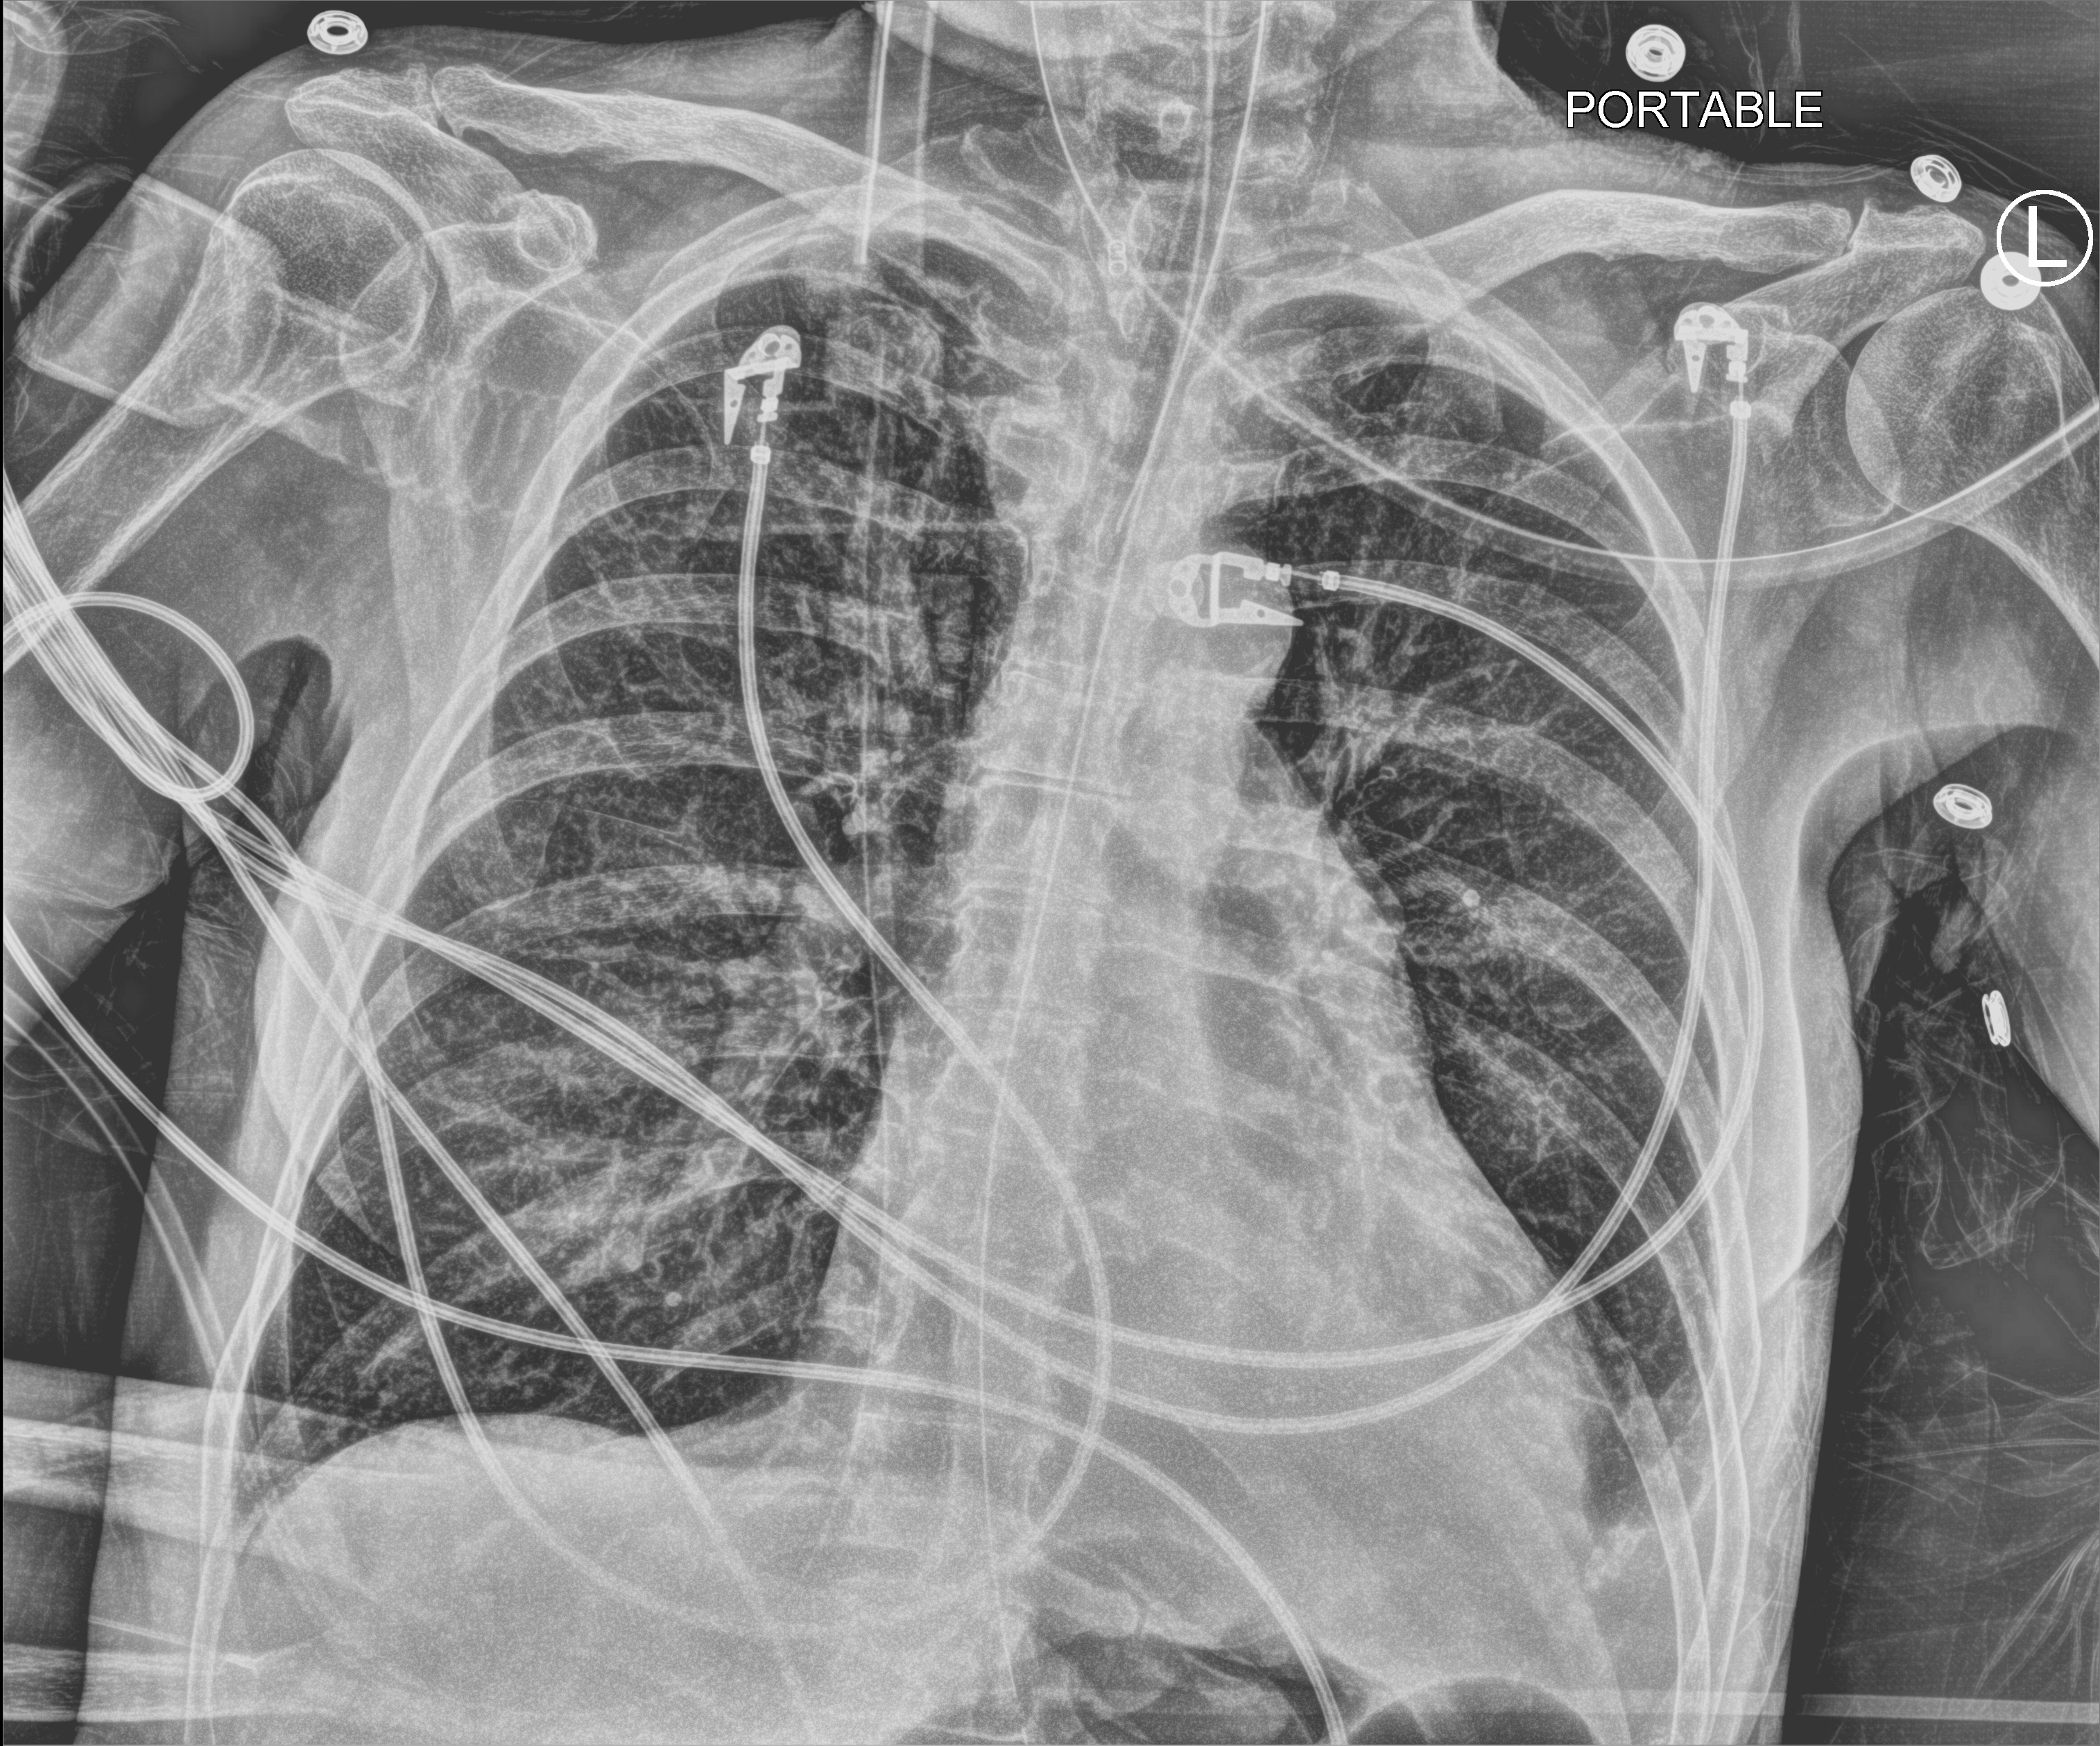
Portable chest radiograph, anteroposterior (AP) projection. Patient hospitalised with COVID-19; female, aged 60–74 years.
Admission-level facts for this patient (not findings on this image; timing relative to this image not recorded): length of hospital stay: 38 days; admitted to intensive care during this hospital stay: yes.